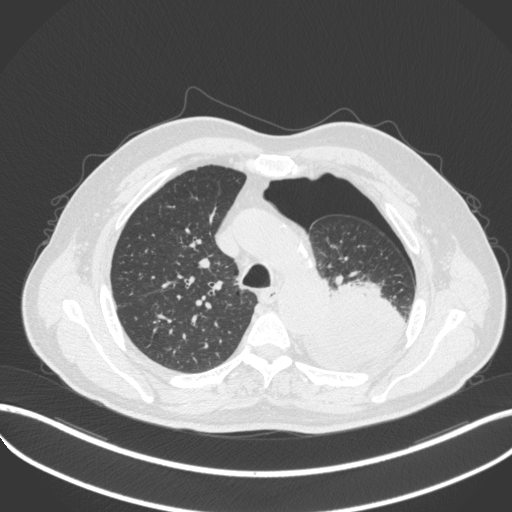
Chest CT, one axial slice; position 374 of 466 along the scan axis; reconstruction kernel B31f; 120 kVp; lung window (W 1500 / L -600 HU); 1 mm slice thickness; 512 × 512 image matrix. Male patient, age 76 years. Case-level facts recorded for this patient, not image findings: clinical TNM (as recorded): T3 N0 M1b.
Annotated regions visible in this slice (rectangle marked by the reading radiologist):
- lung tumour (recorded histology: adenocarcinoma): bounding box <301,277,409,378> (left, top, right, bottom; pixels)